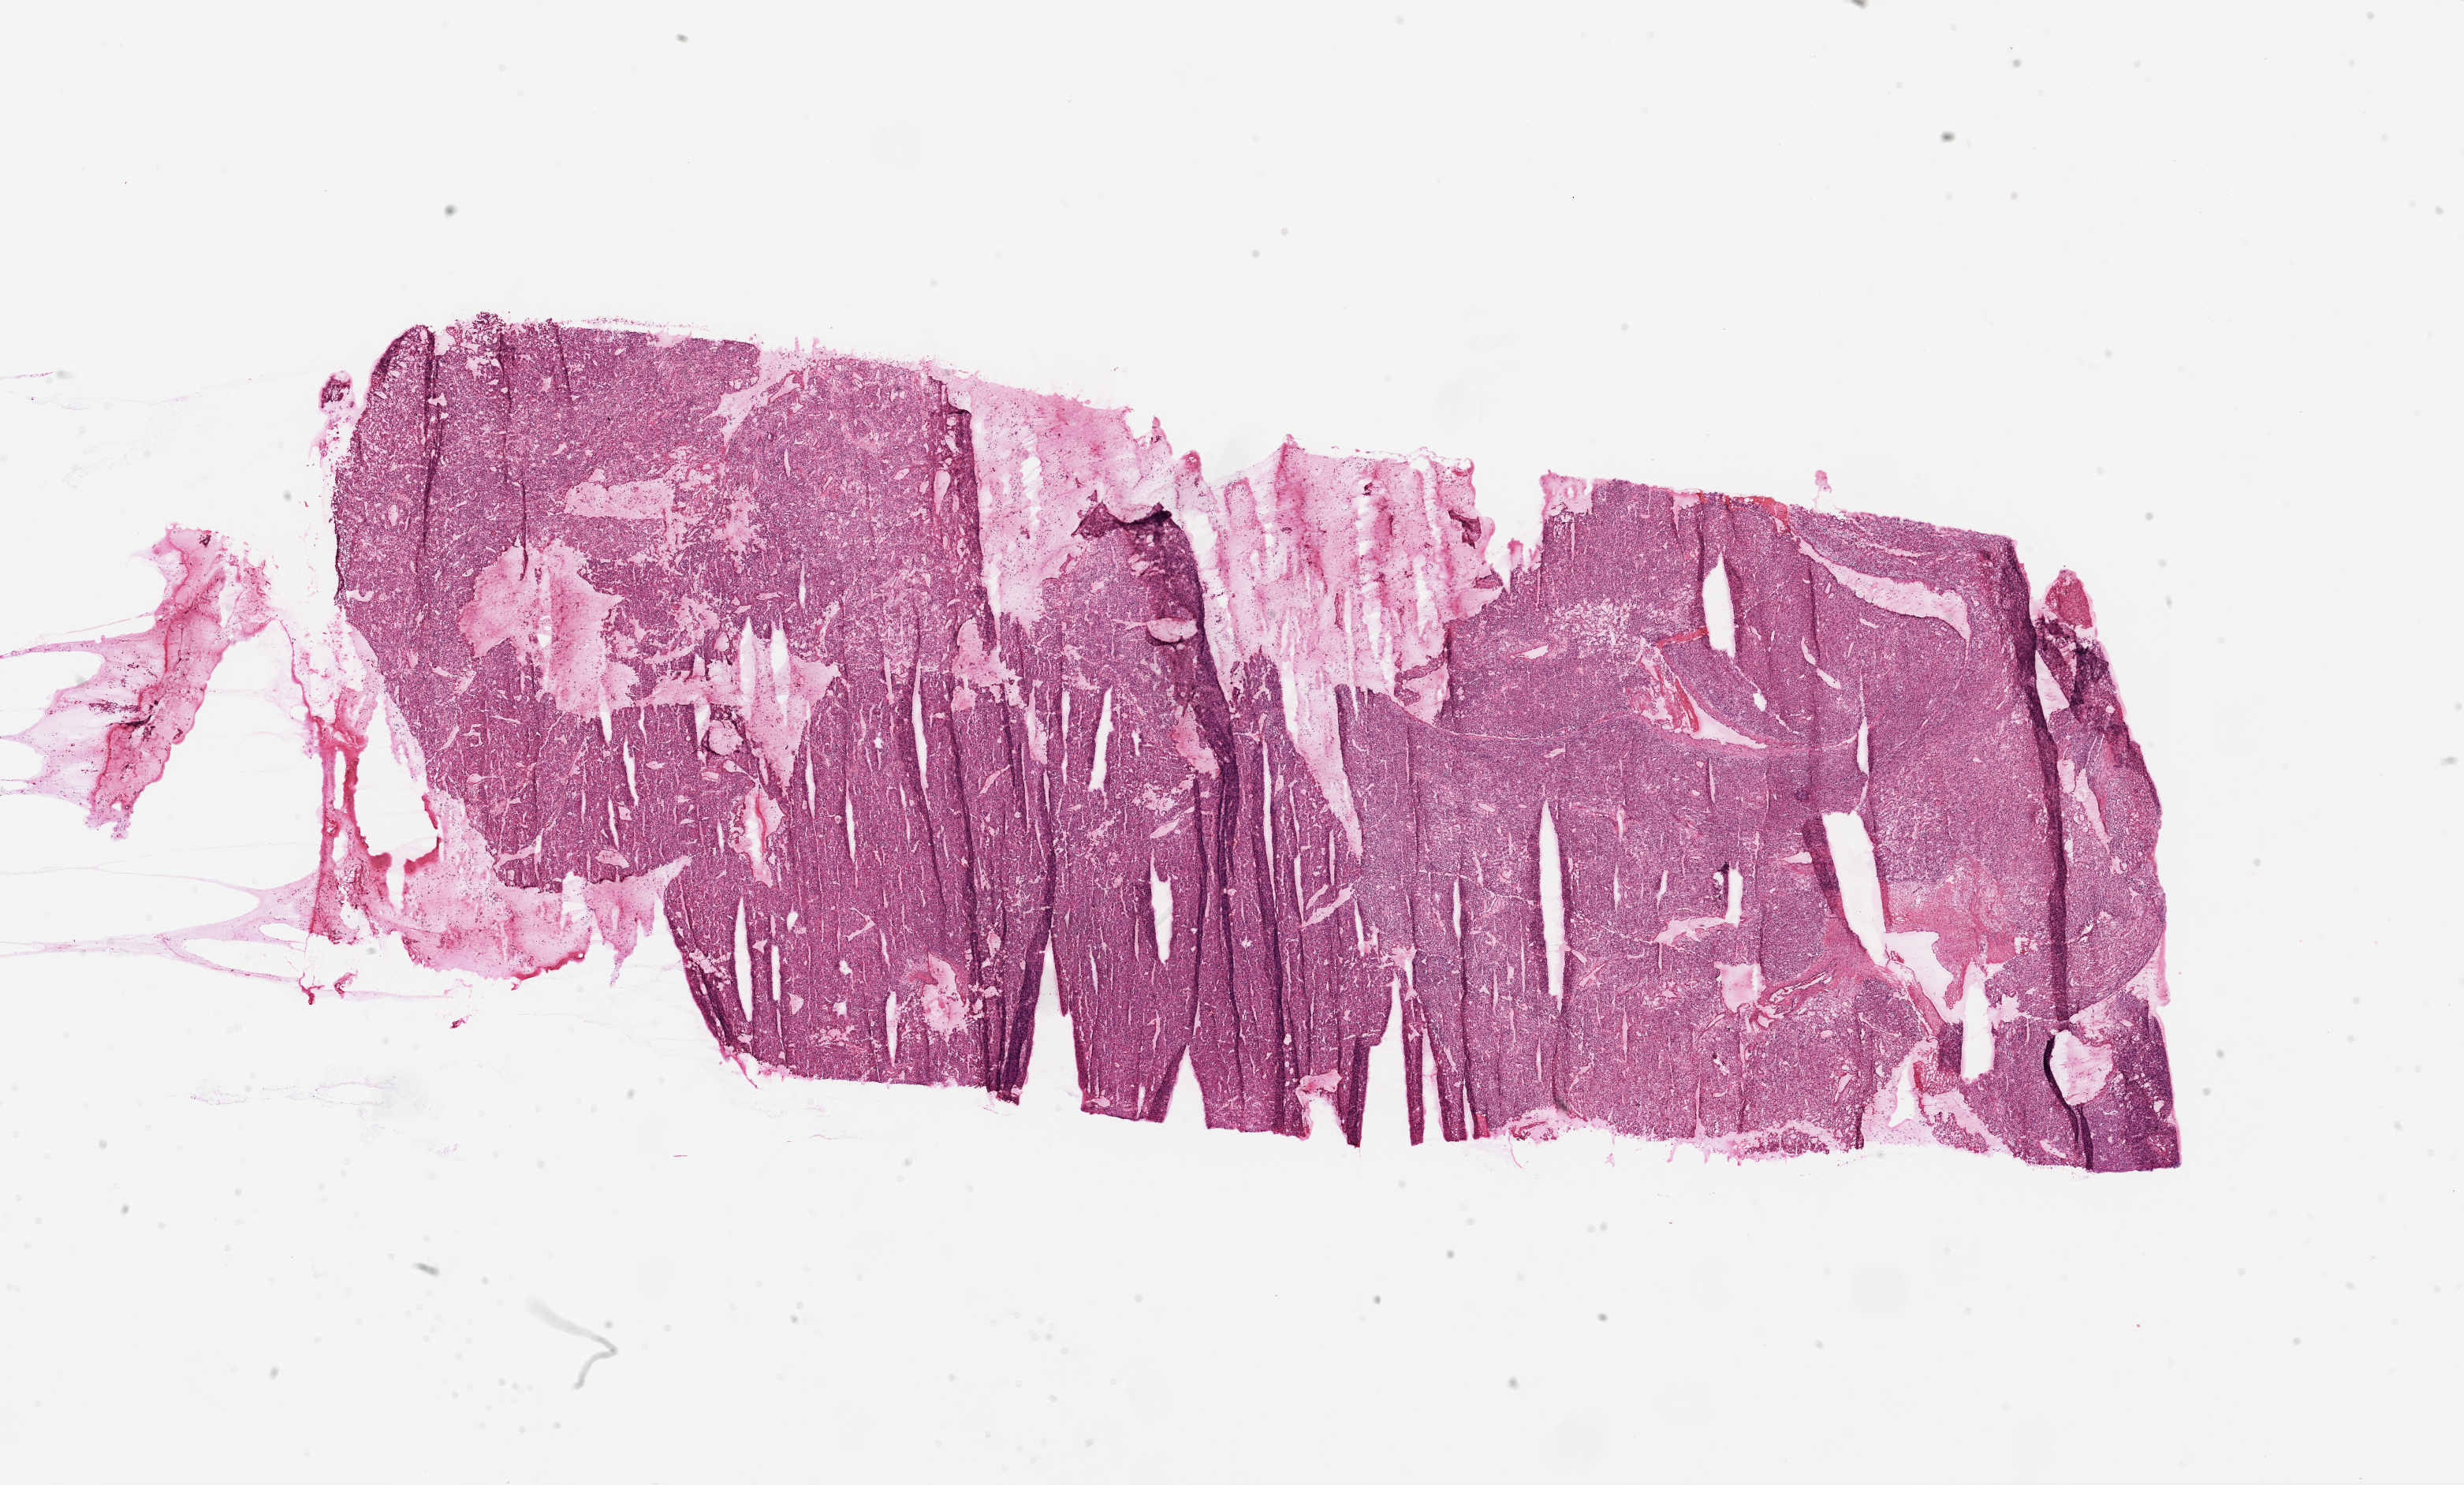
Hematoxylin and eosin (H&E) stained whole-slide image — low-resolution overview of the scanned area, about 25.1 x 15.1 mm. Frozen section. Kidney, primary tumour sample. Patient: female, age at initial diagnosis 48 years. Histologic grade: G3 (poorly differentiated). Pathologist review of this section (percent, as recorded): tumour cells 95%, tumour nuclei 85%, normal cells 0%, stromal cells 5%, necrosis 0%.
- AJCC pathologic stage: IV
- laterality: left
- diagnosis: Clear cell adenocarcinoma, NOS